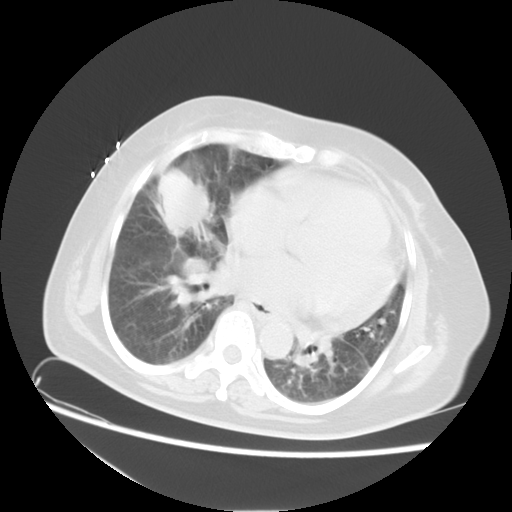
Chest CT, one axial slice. Reconstruction kernel STANDARD. Lung window (W 1500 / L -600 HU). 512 × 512 image matrix, field of view 350 × 350 mm. Female patient, age 67 years. Case-level facts recorded for this patient, not image findings: clinical TNM (as recorded): T2a N3 M1a.
Outlined on this slice (bounding box drawn by a radiologist):
- lung tumour (recorded histology: adenocarcinoma): bounding box <156,174,210,237> (left, top, right, bottom; pixels)